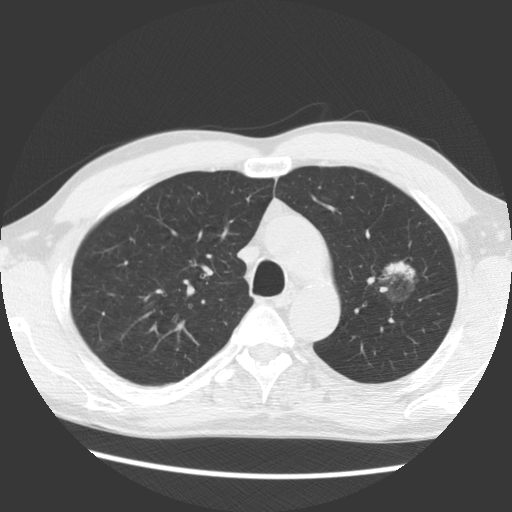
Axial slice from a low-dose chest CT screening exam, first (baseline) screen, lung window (W 1500 / L -600 HU), standard (soft-tissue) reconstruction kernel (STANDARD), slice 99 of 138 in the series. Male participant, aged 61 years at enrolment. Former smoker at enrolment.
- Expert-annotated lung lesion, bounding box (x1, y1, x2, y2) in pixels: (356, 239, 441, 314).
- Reader record for this screening exam (exam-level; its link to the box is not recorded): non-calcified nodule or mass ≥4 mm, left upper lobe, 17 × 14 mm, soft tissue attenuation.
- Lung cancer was diagnosed 1061 days after this screen: bronchiolo-alveolar adenocarcinoma, NOS, left upper lobe, well differentiated (G1), stage IB (AJCC 6th edition), 44 mm at pathology.